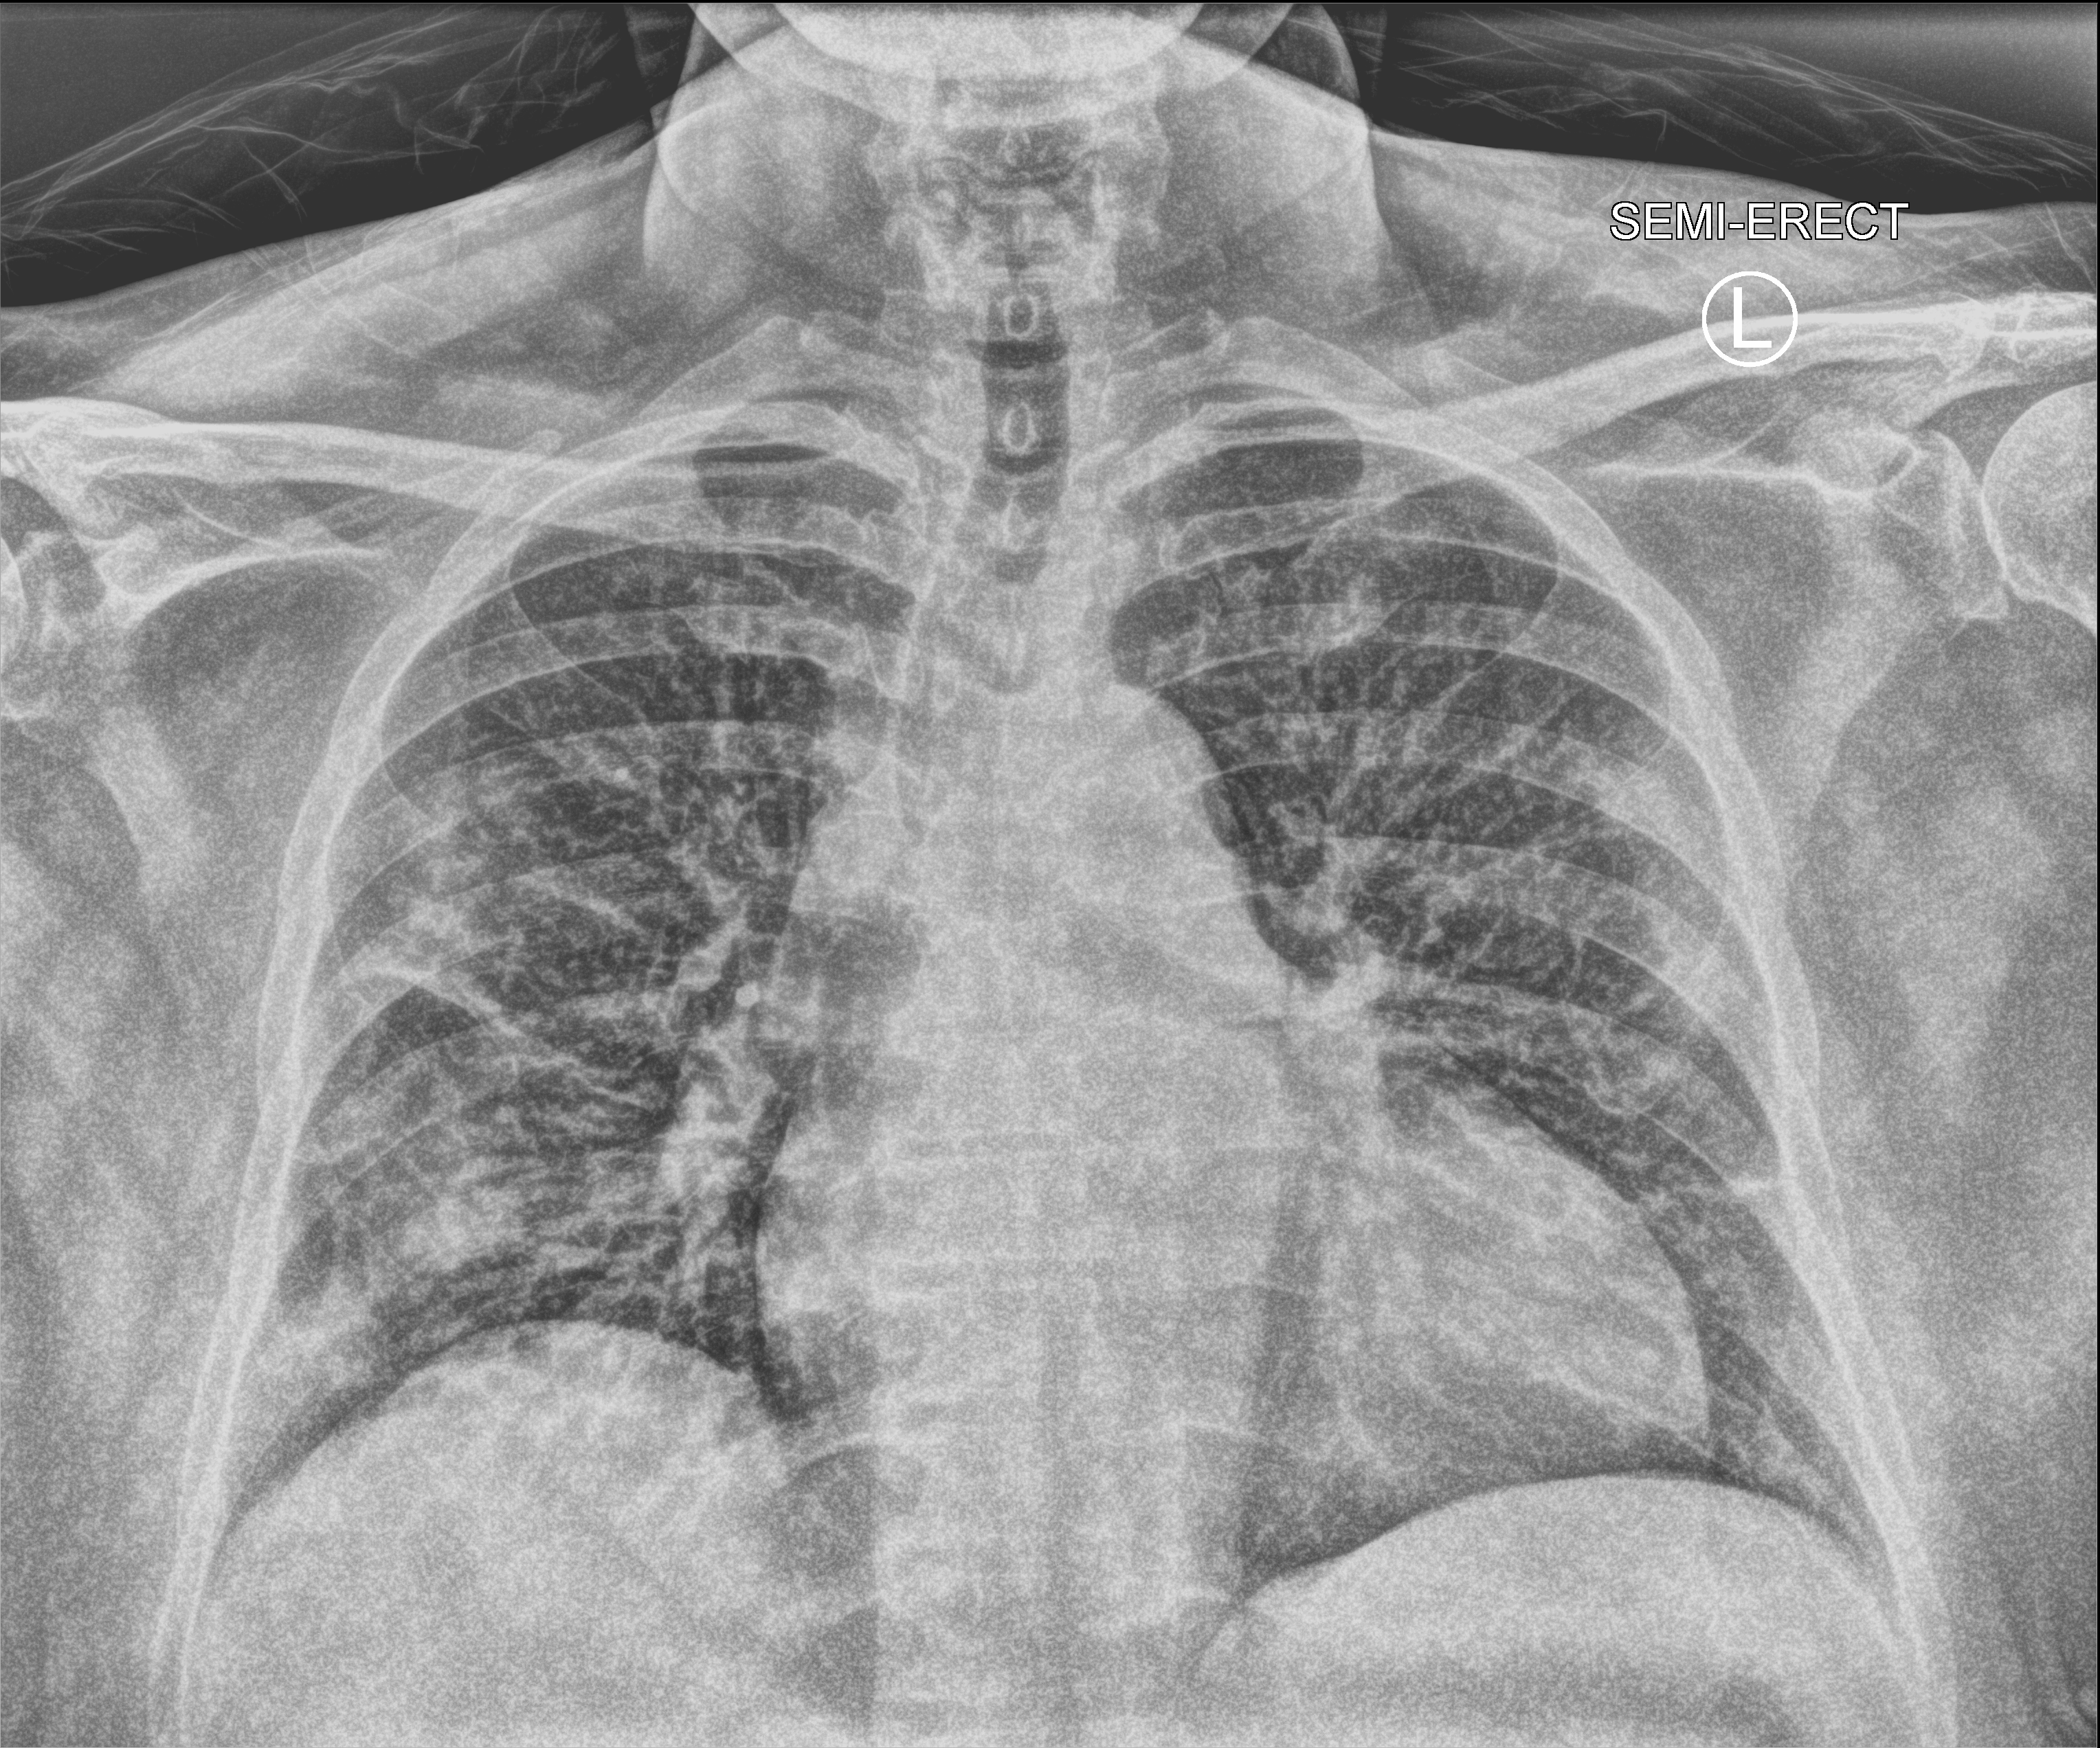
Portable chest radiograph; anteroposterior (AP) projection. Female patient hospitalised with COVID-19, age 60–74 years.
Hospital-stay facts (about this admission, not read from this image; timing relative to this image not recorded): mechanically ventilated during this hospital stay: no; chronic kidney disease (admission record): no.